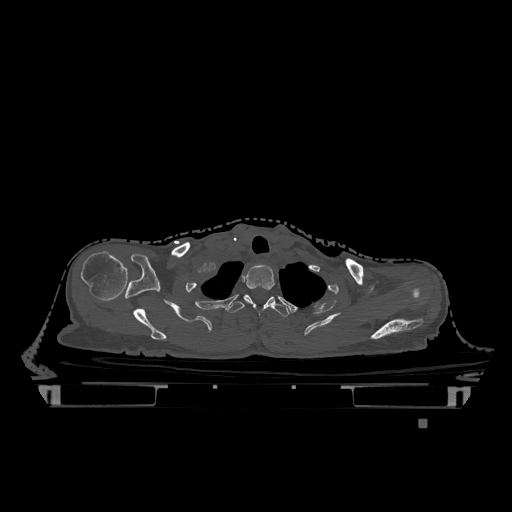
CT including the spine, one axial slice; slice 981 of 1317 in the series (ordered by position); bone window (W 1800 / L 400 HU); 512 × 512 image matrix, field of view 500 × 500 mm. Patient: female, 74 years. From the clinical record (not read from this slice): primary cancer: lung; vertebrae with lytic lesions (as recorded): T1, T4, T5, T6, L4, L5.
Structures marked on this image (semi-automatic segmentation, software-assisted and operator-edited):
- T1 vertebra: box from (x=244, y=265) to (x=275, y=304) px
- T2 vertebra: (x=227, y=294)–(x=290, y=317)